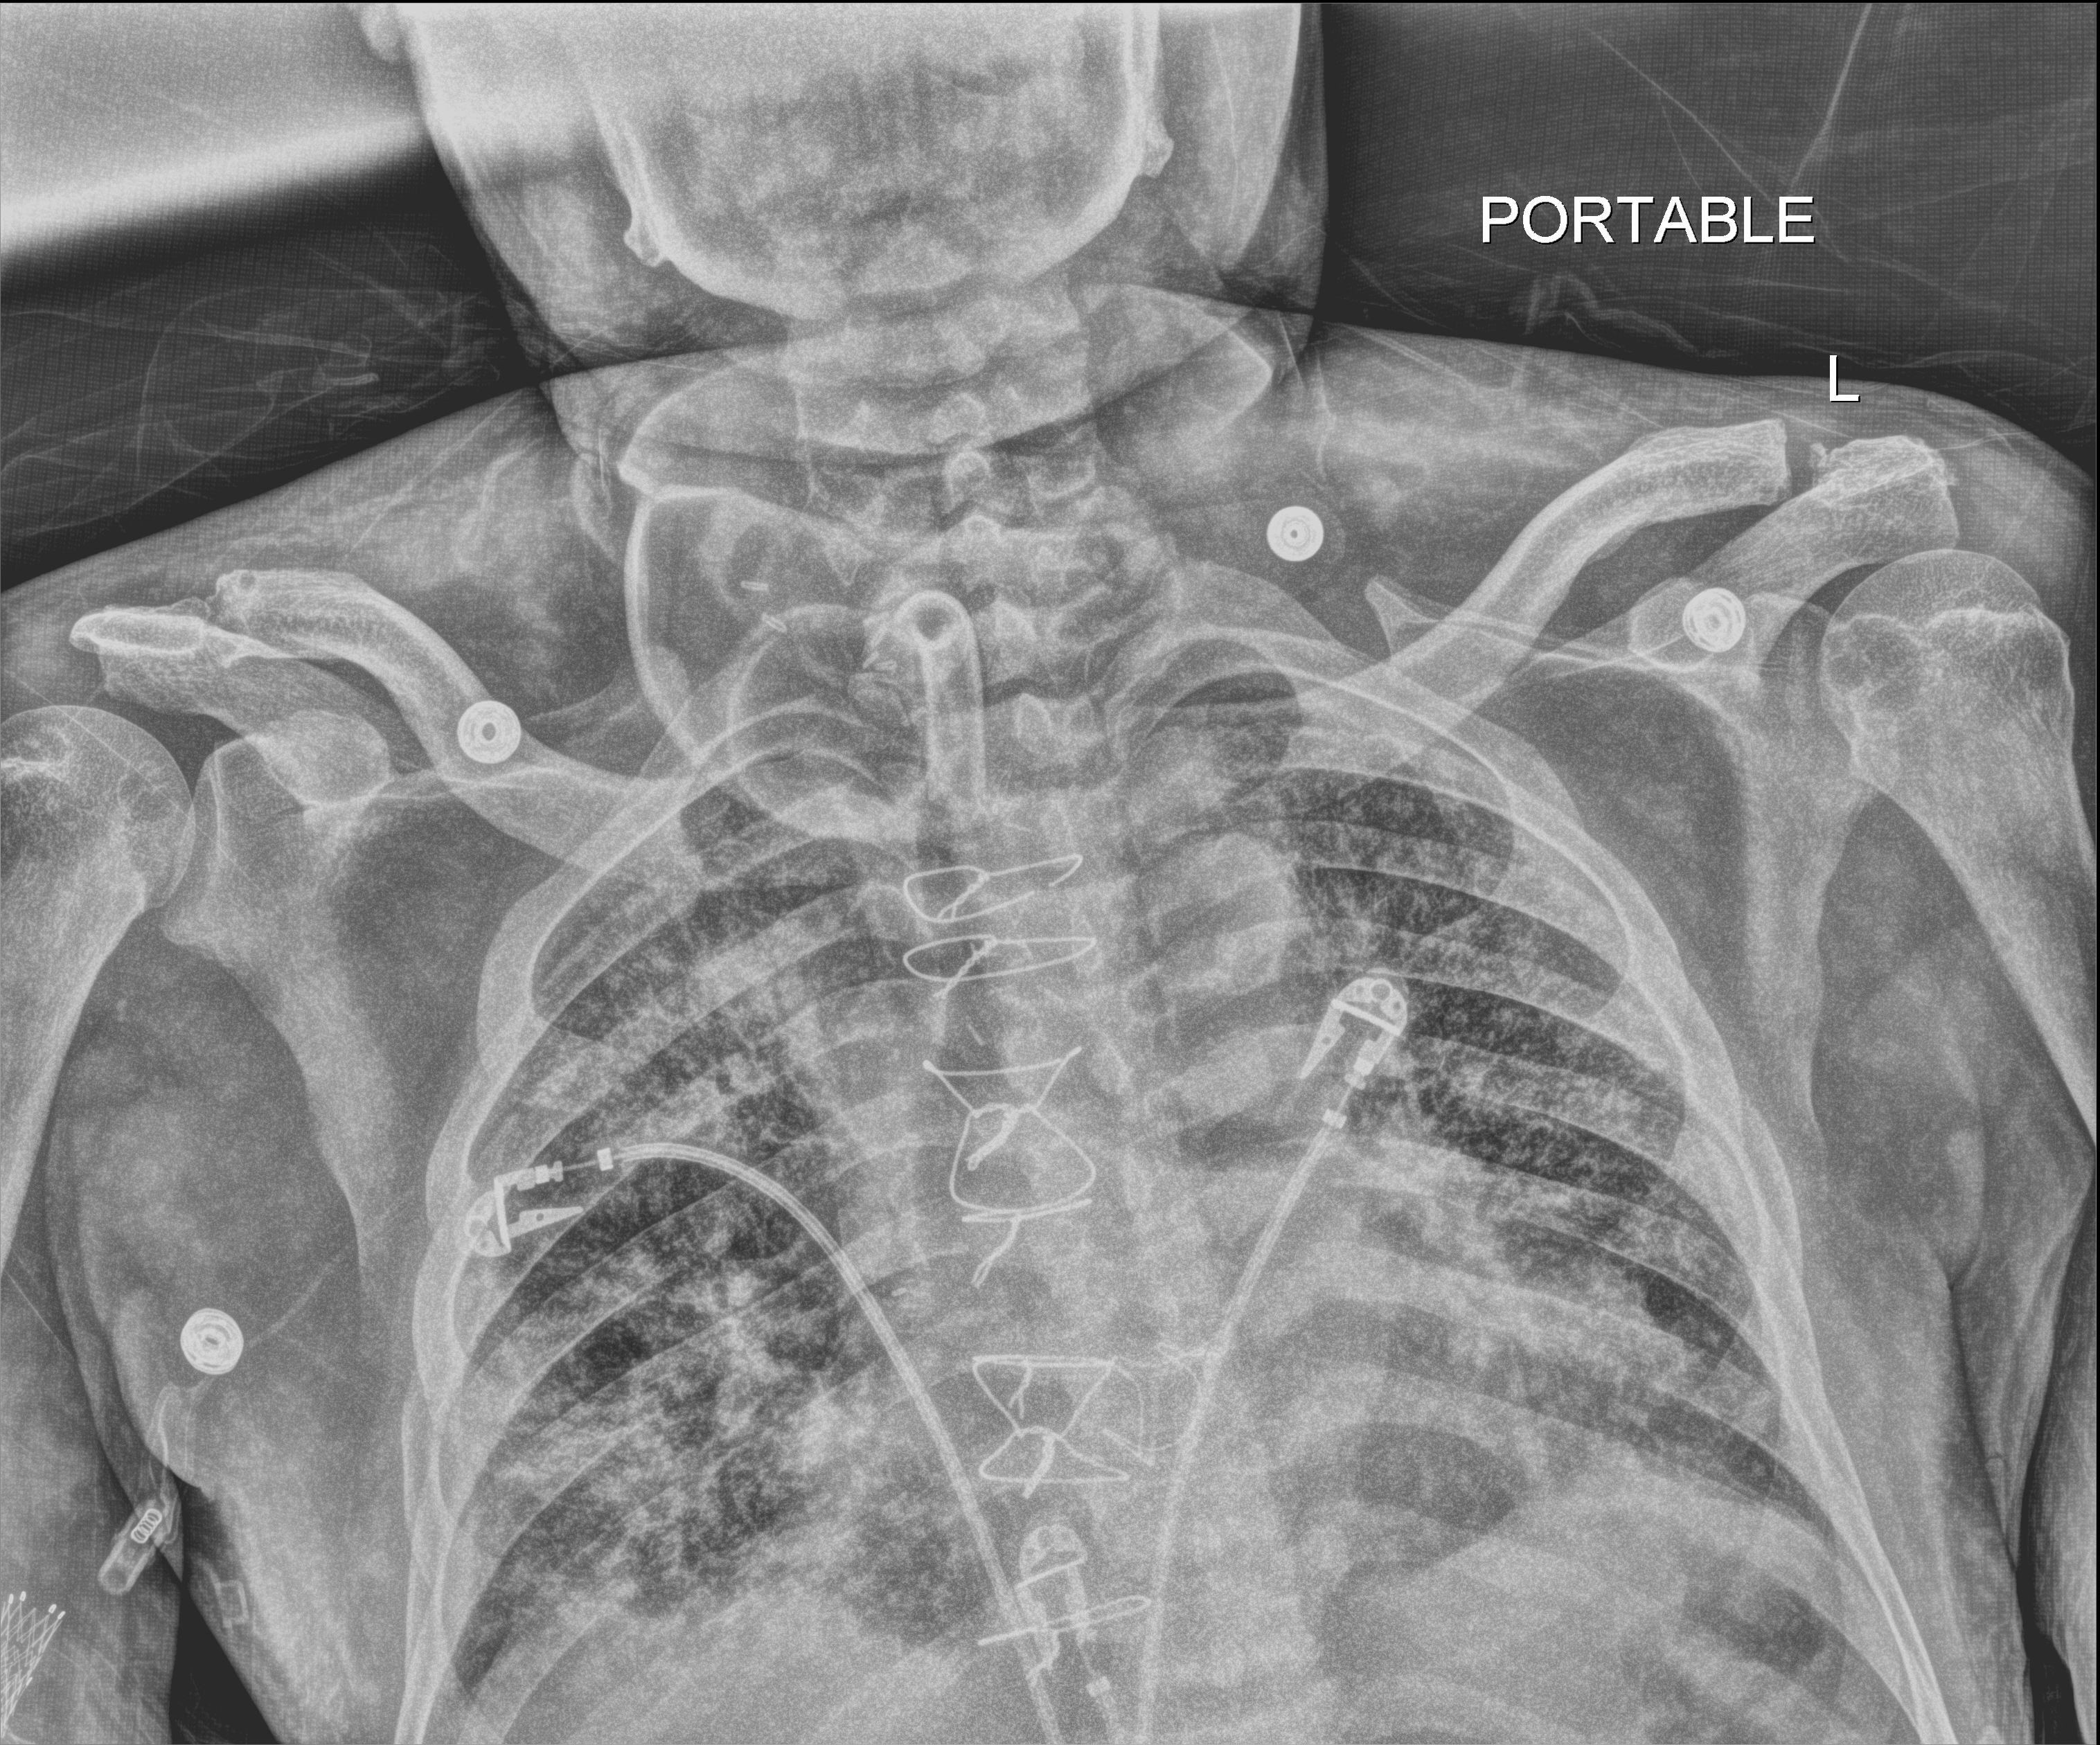
Portable chest radiograph. Patient hospitalised with COVID-19; male, aged 60–74 years.
Admission-level facts for this patient (not findings on this image; timing relative to this image not recorded):
- admitted to intensive care during this hospital stay: yes
- diabetes (admission record): no